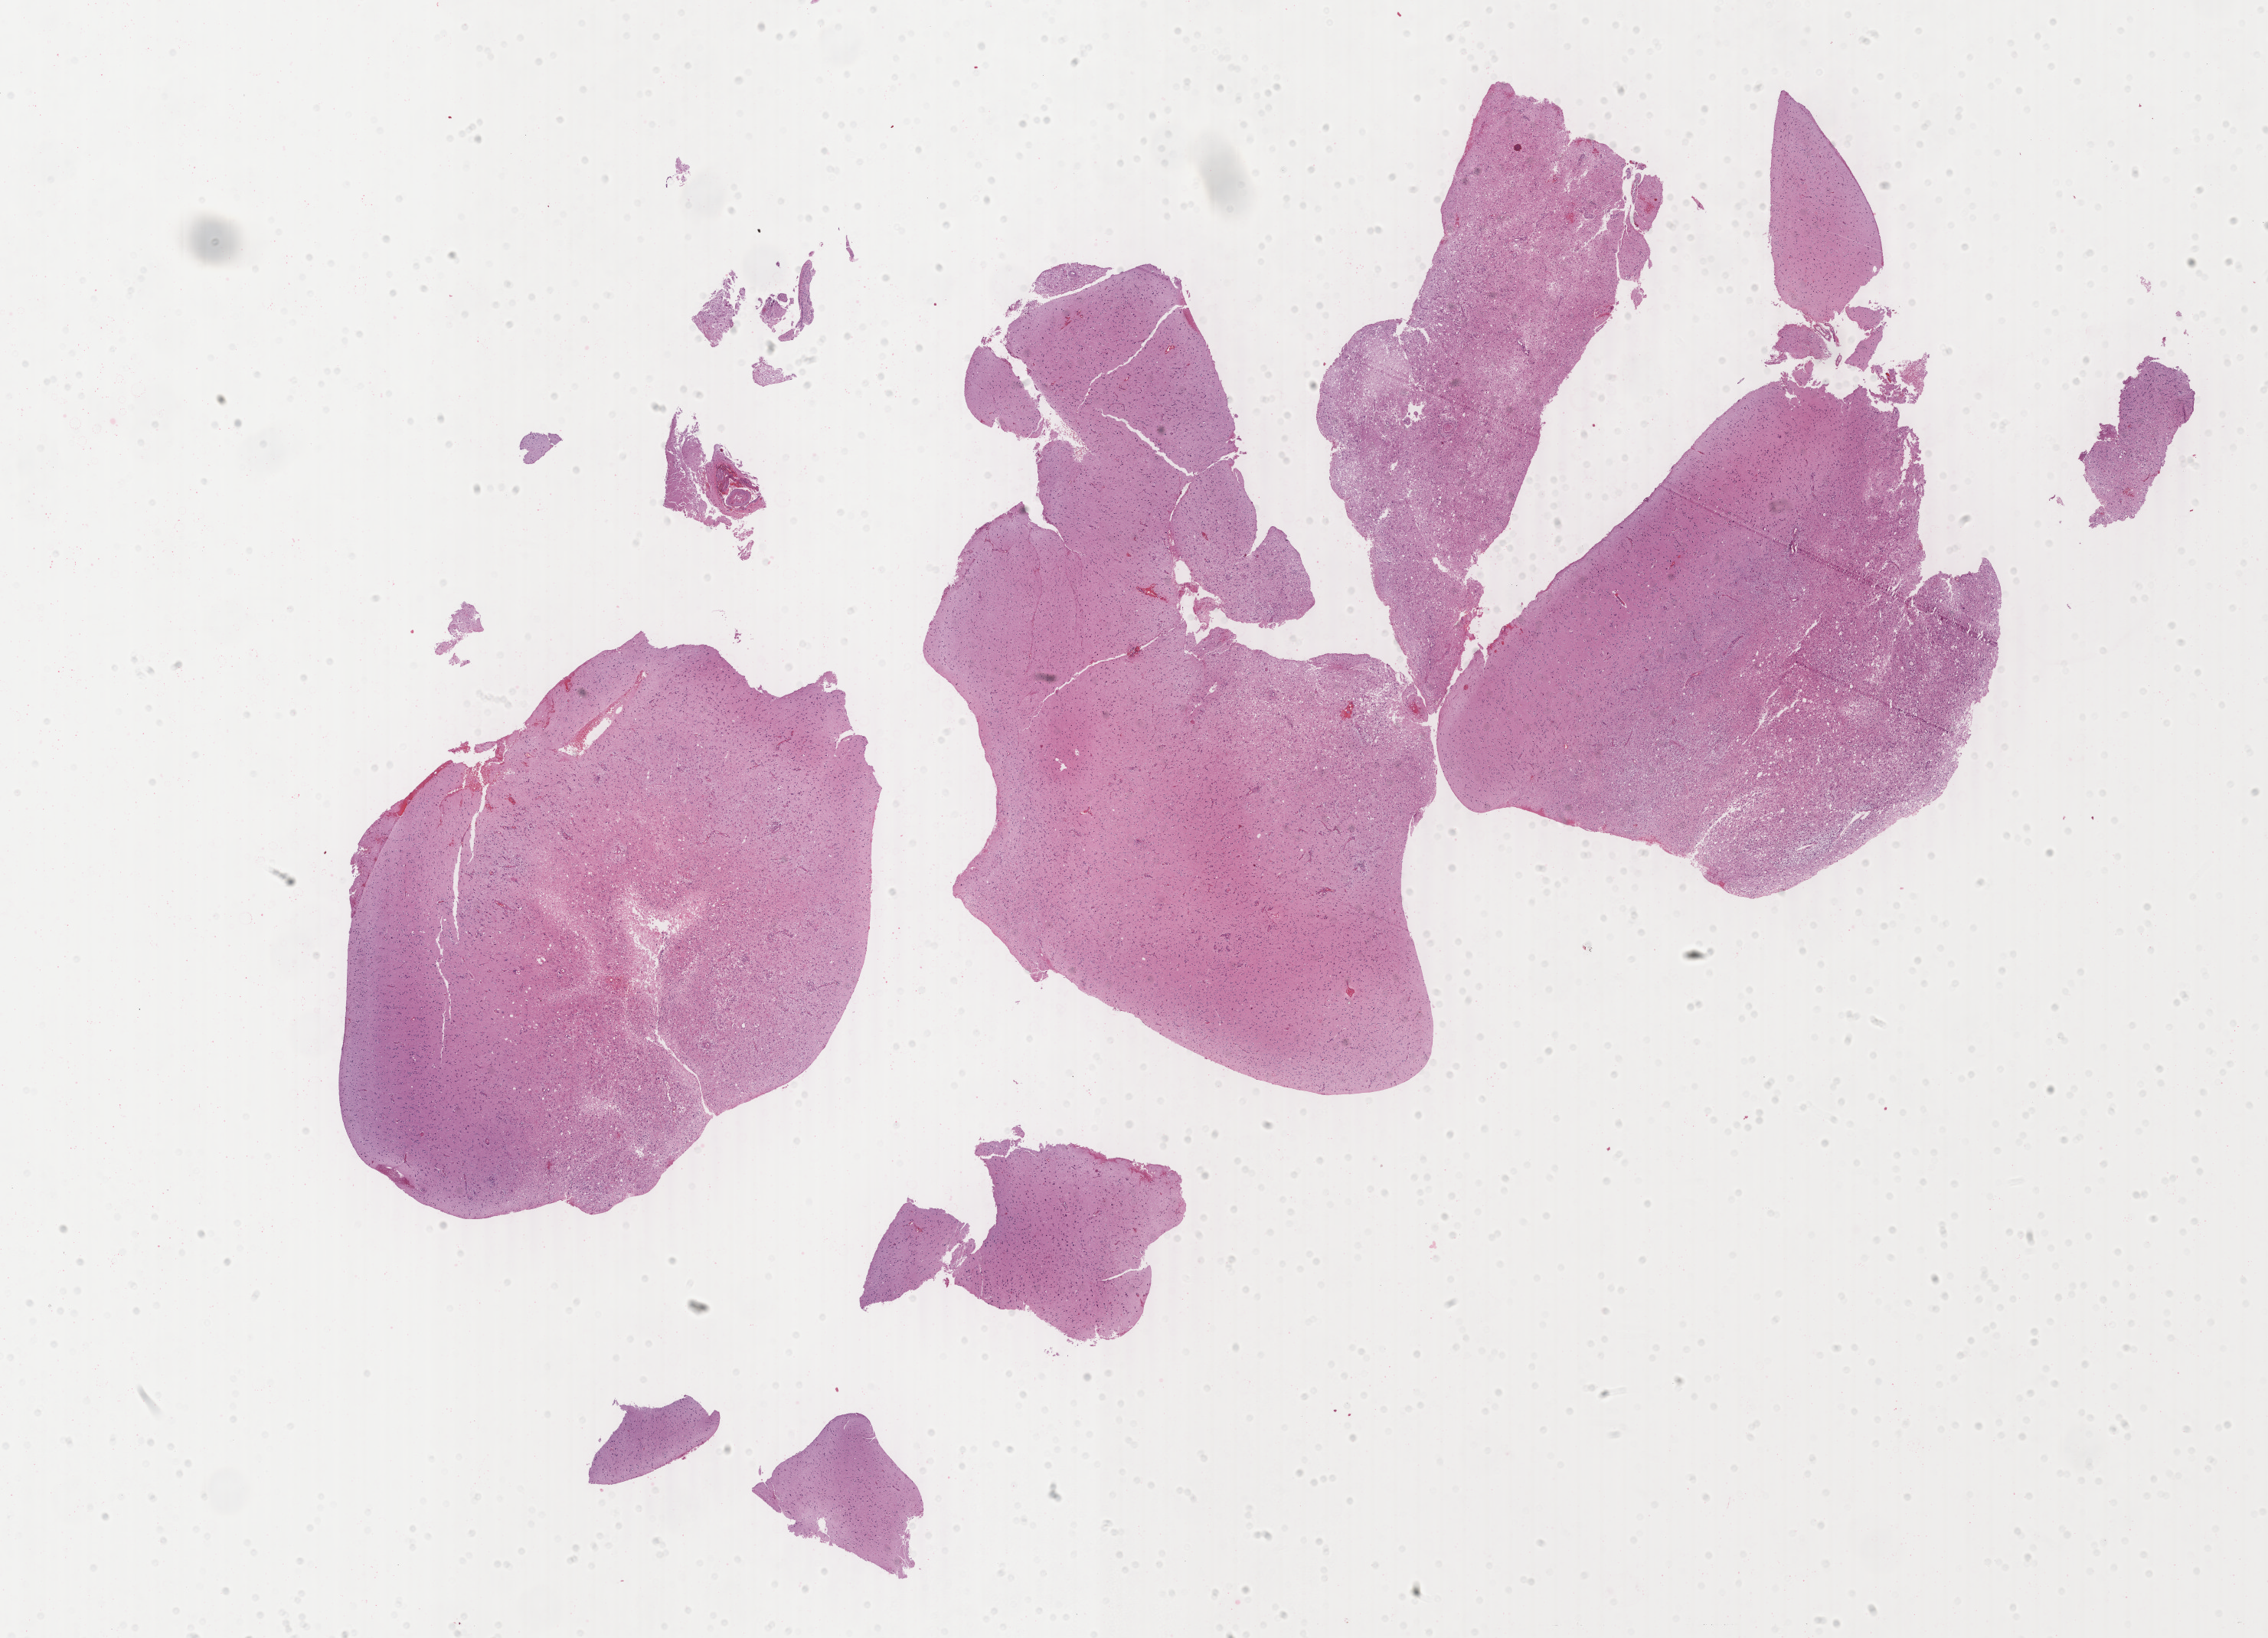
H&E-stained whole-slide image — whole scanned area (about 23.6 x 17.0 mm) shown as a low-resolution overview. Formalin-fixed paraffin-embedded (FFPE) diagnostic section. Brain, primary tumour sample. Female, age 65 years at initial diagnosis.
Pathologic diagnosis: Glioblastoma.